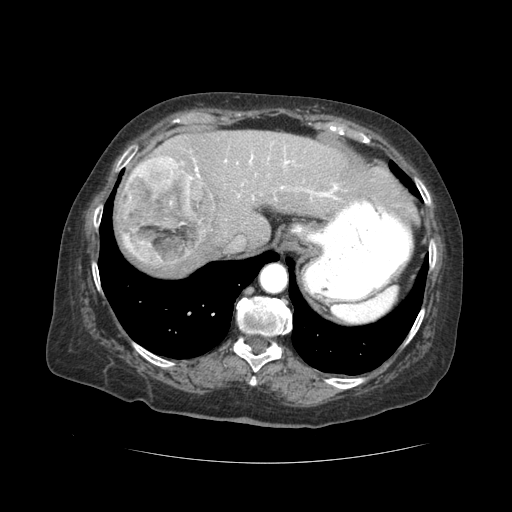
Contrast-enhanced abdominal CT (liver protocol), one axial slice. Slice 36 of 59 in the series (ordered by position). Soft-tissue window (W 400 / L 40 HU). 2.5 mm slice thickness. 512 × 512 image matrix, field of view 380 × 380 mm. From the clinical record (not read from this slice): diagnosis: hepatocellular carcinoma (patient treated with transarterial chemoembolisation; whether this scan precedes or follows treatment is not stated here); TNM stage (as recorded): Stage-I; Child-Pugh class: A; tumour nodularity: uninodular.
Structures marked on this image (semi-automatically segmented with operator editing):
- abdominal aorta: box from (x=262, y=265) to (x=287, y=292) px
- liver parenchyma outside the tumour (the mass and vessels are separate outlines, so this box may not span the whole liver): (x=114, y=130)–(x=414, y=276)
- mass: (x=120, y=156)–(x=215, y=266)
- liver vessels: (x=181, y=143)–(x=384, y=212)